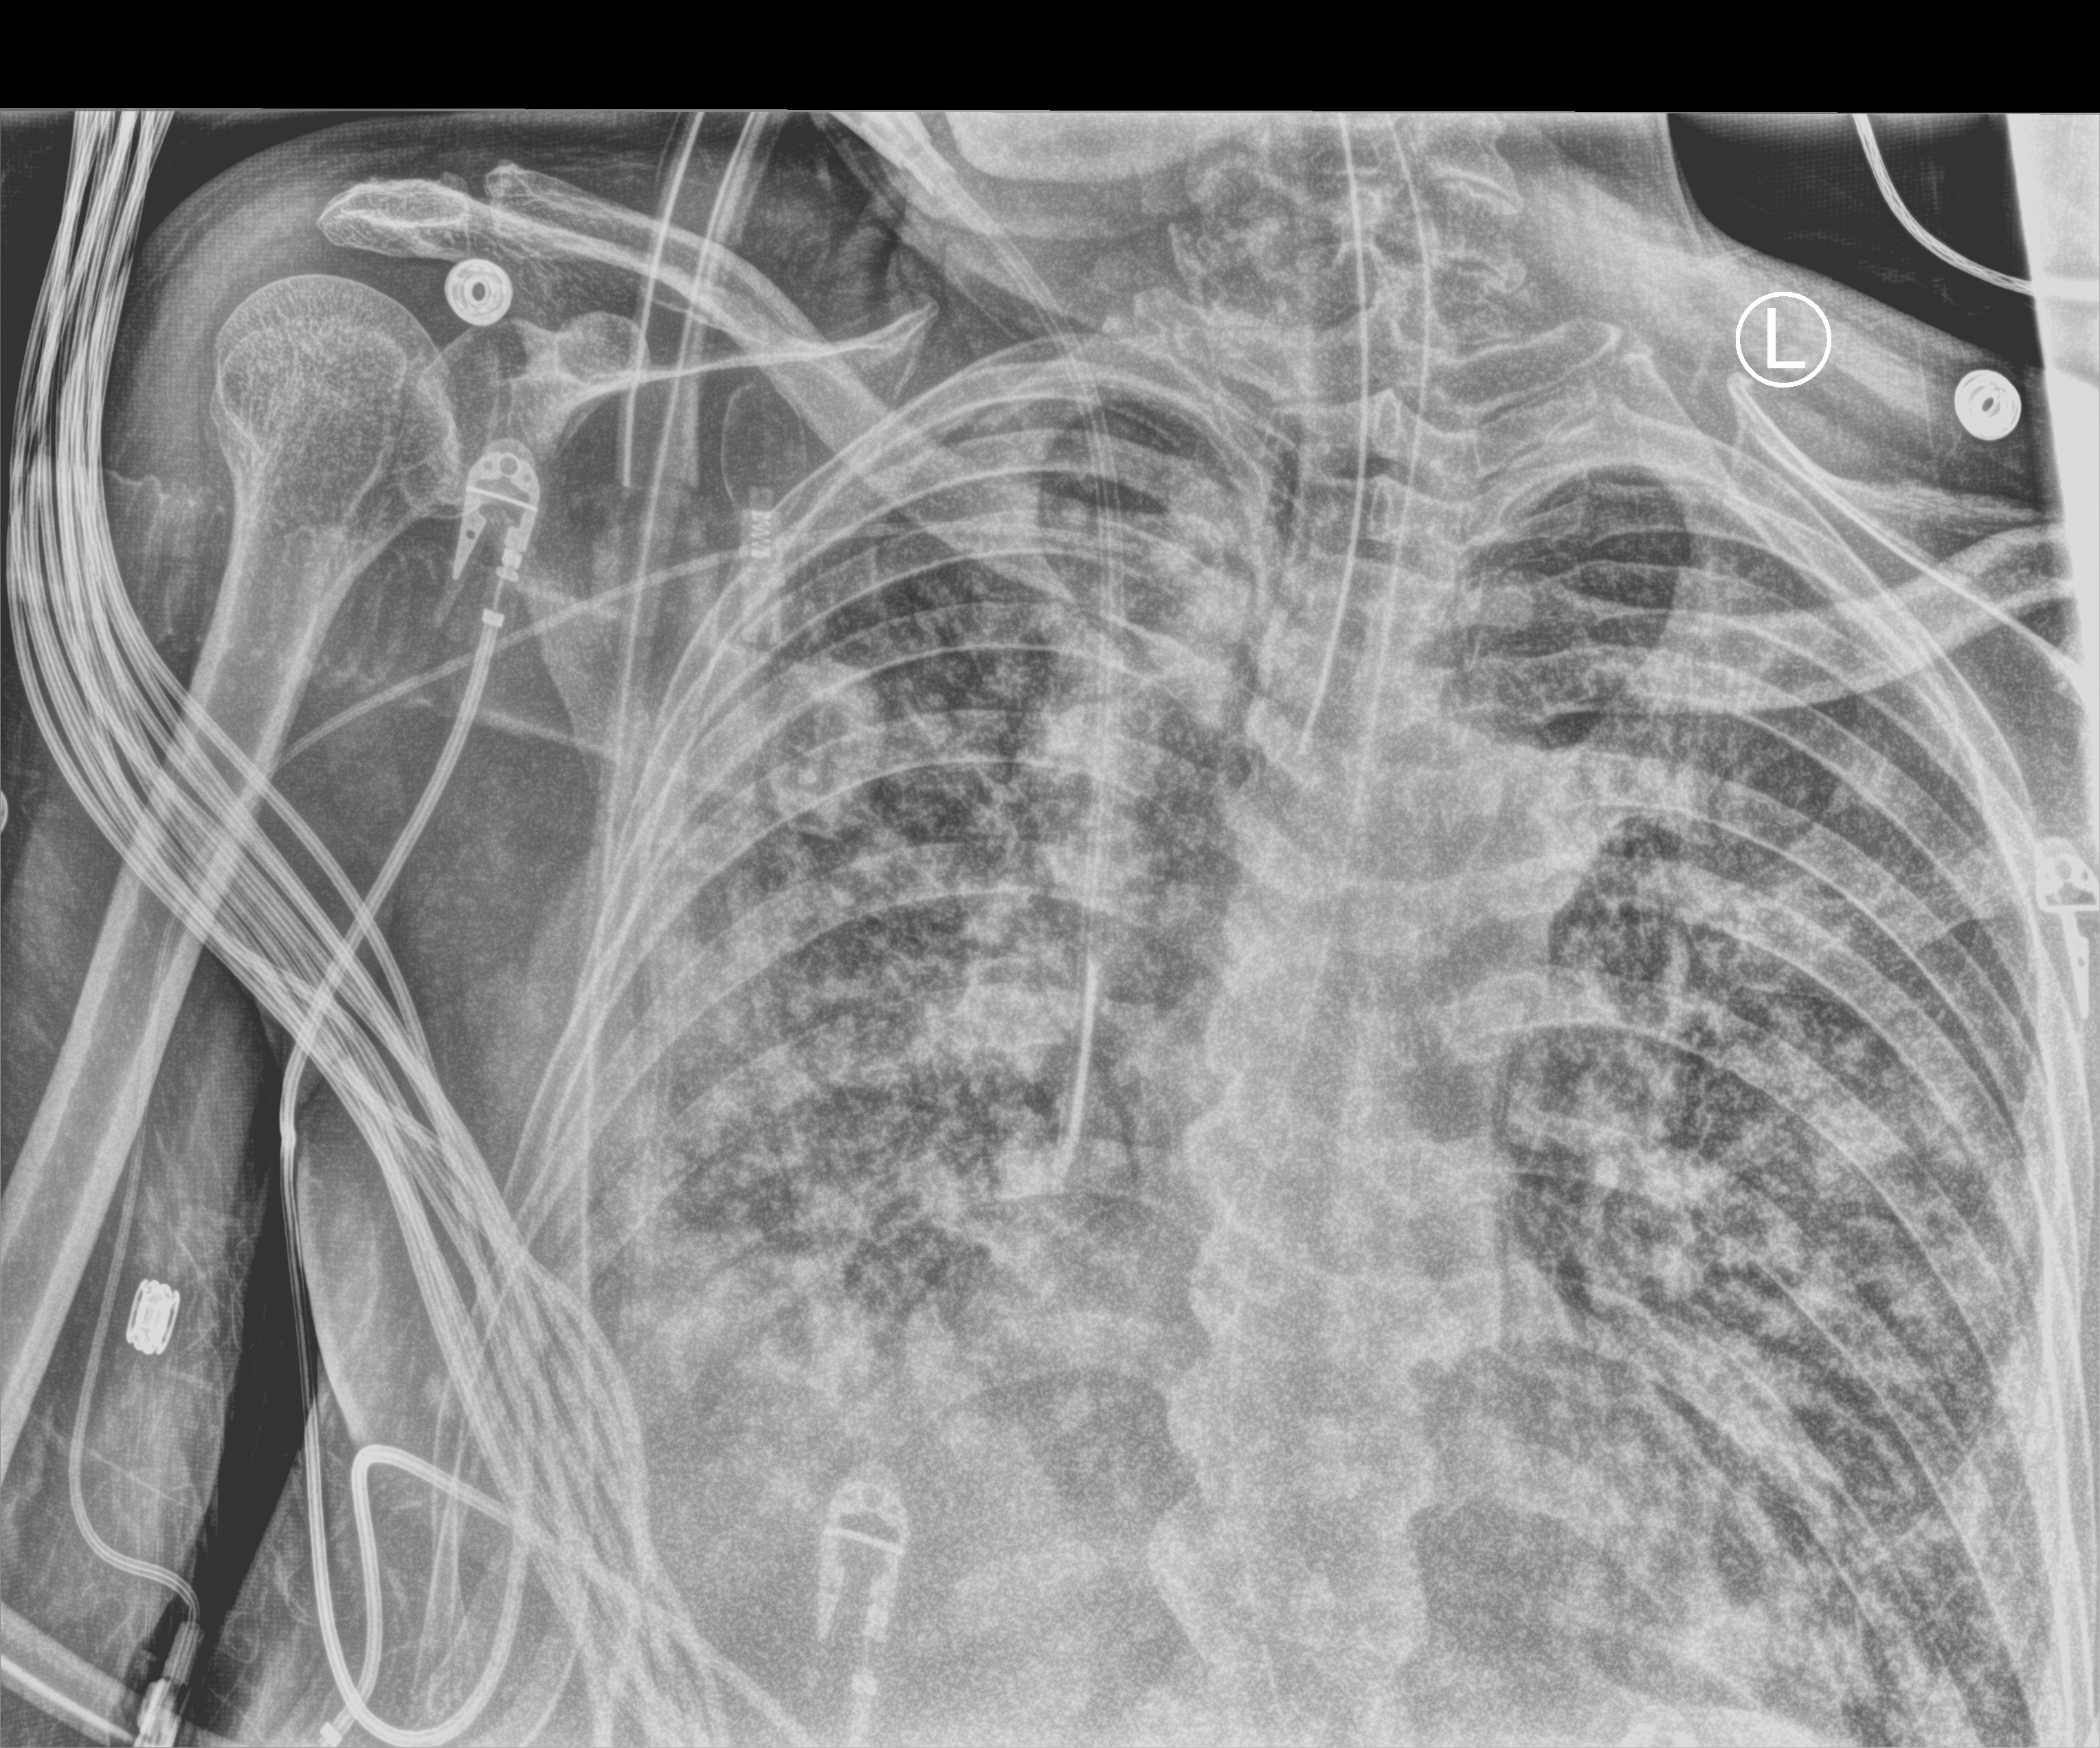
Bedside chest radiograph (computed radiography); anteroposterior (AP) projection. Male patient hospitalised with COVID-19, age 60–74 years.
From the hospital-stay record, not from the radiograph (when in the stay this image was taken is not recorded): chronic kidney disease (admission record): no.